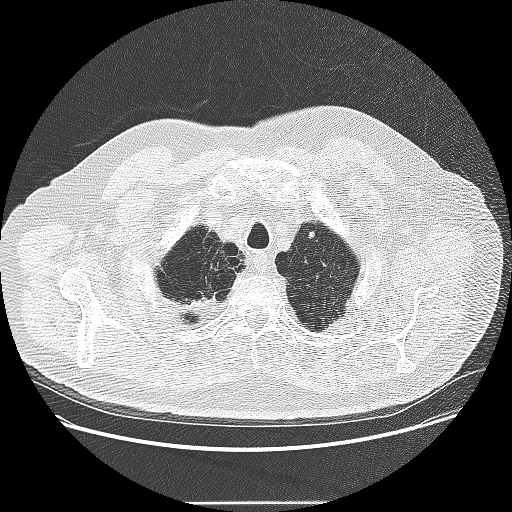
Low-dose screening chest CT, one axial slice. Slice 223 of 265 in the series (ordered by position). Reconstruction kernel LUNG. 120 kVp. Lung window (W 1500 / L -600 HU). 2.5 mm slice thickness. 512 × 512 image matrix, field of view 400 × 400 mm.
Outlined on this slice (expert manual segmentation):
- lesion 1 (tumor, upper lobe of left lung): bounding box (x1, y1, x2, y2) in pixels: (309, 230, 315, 239)